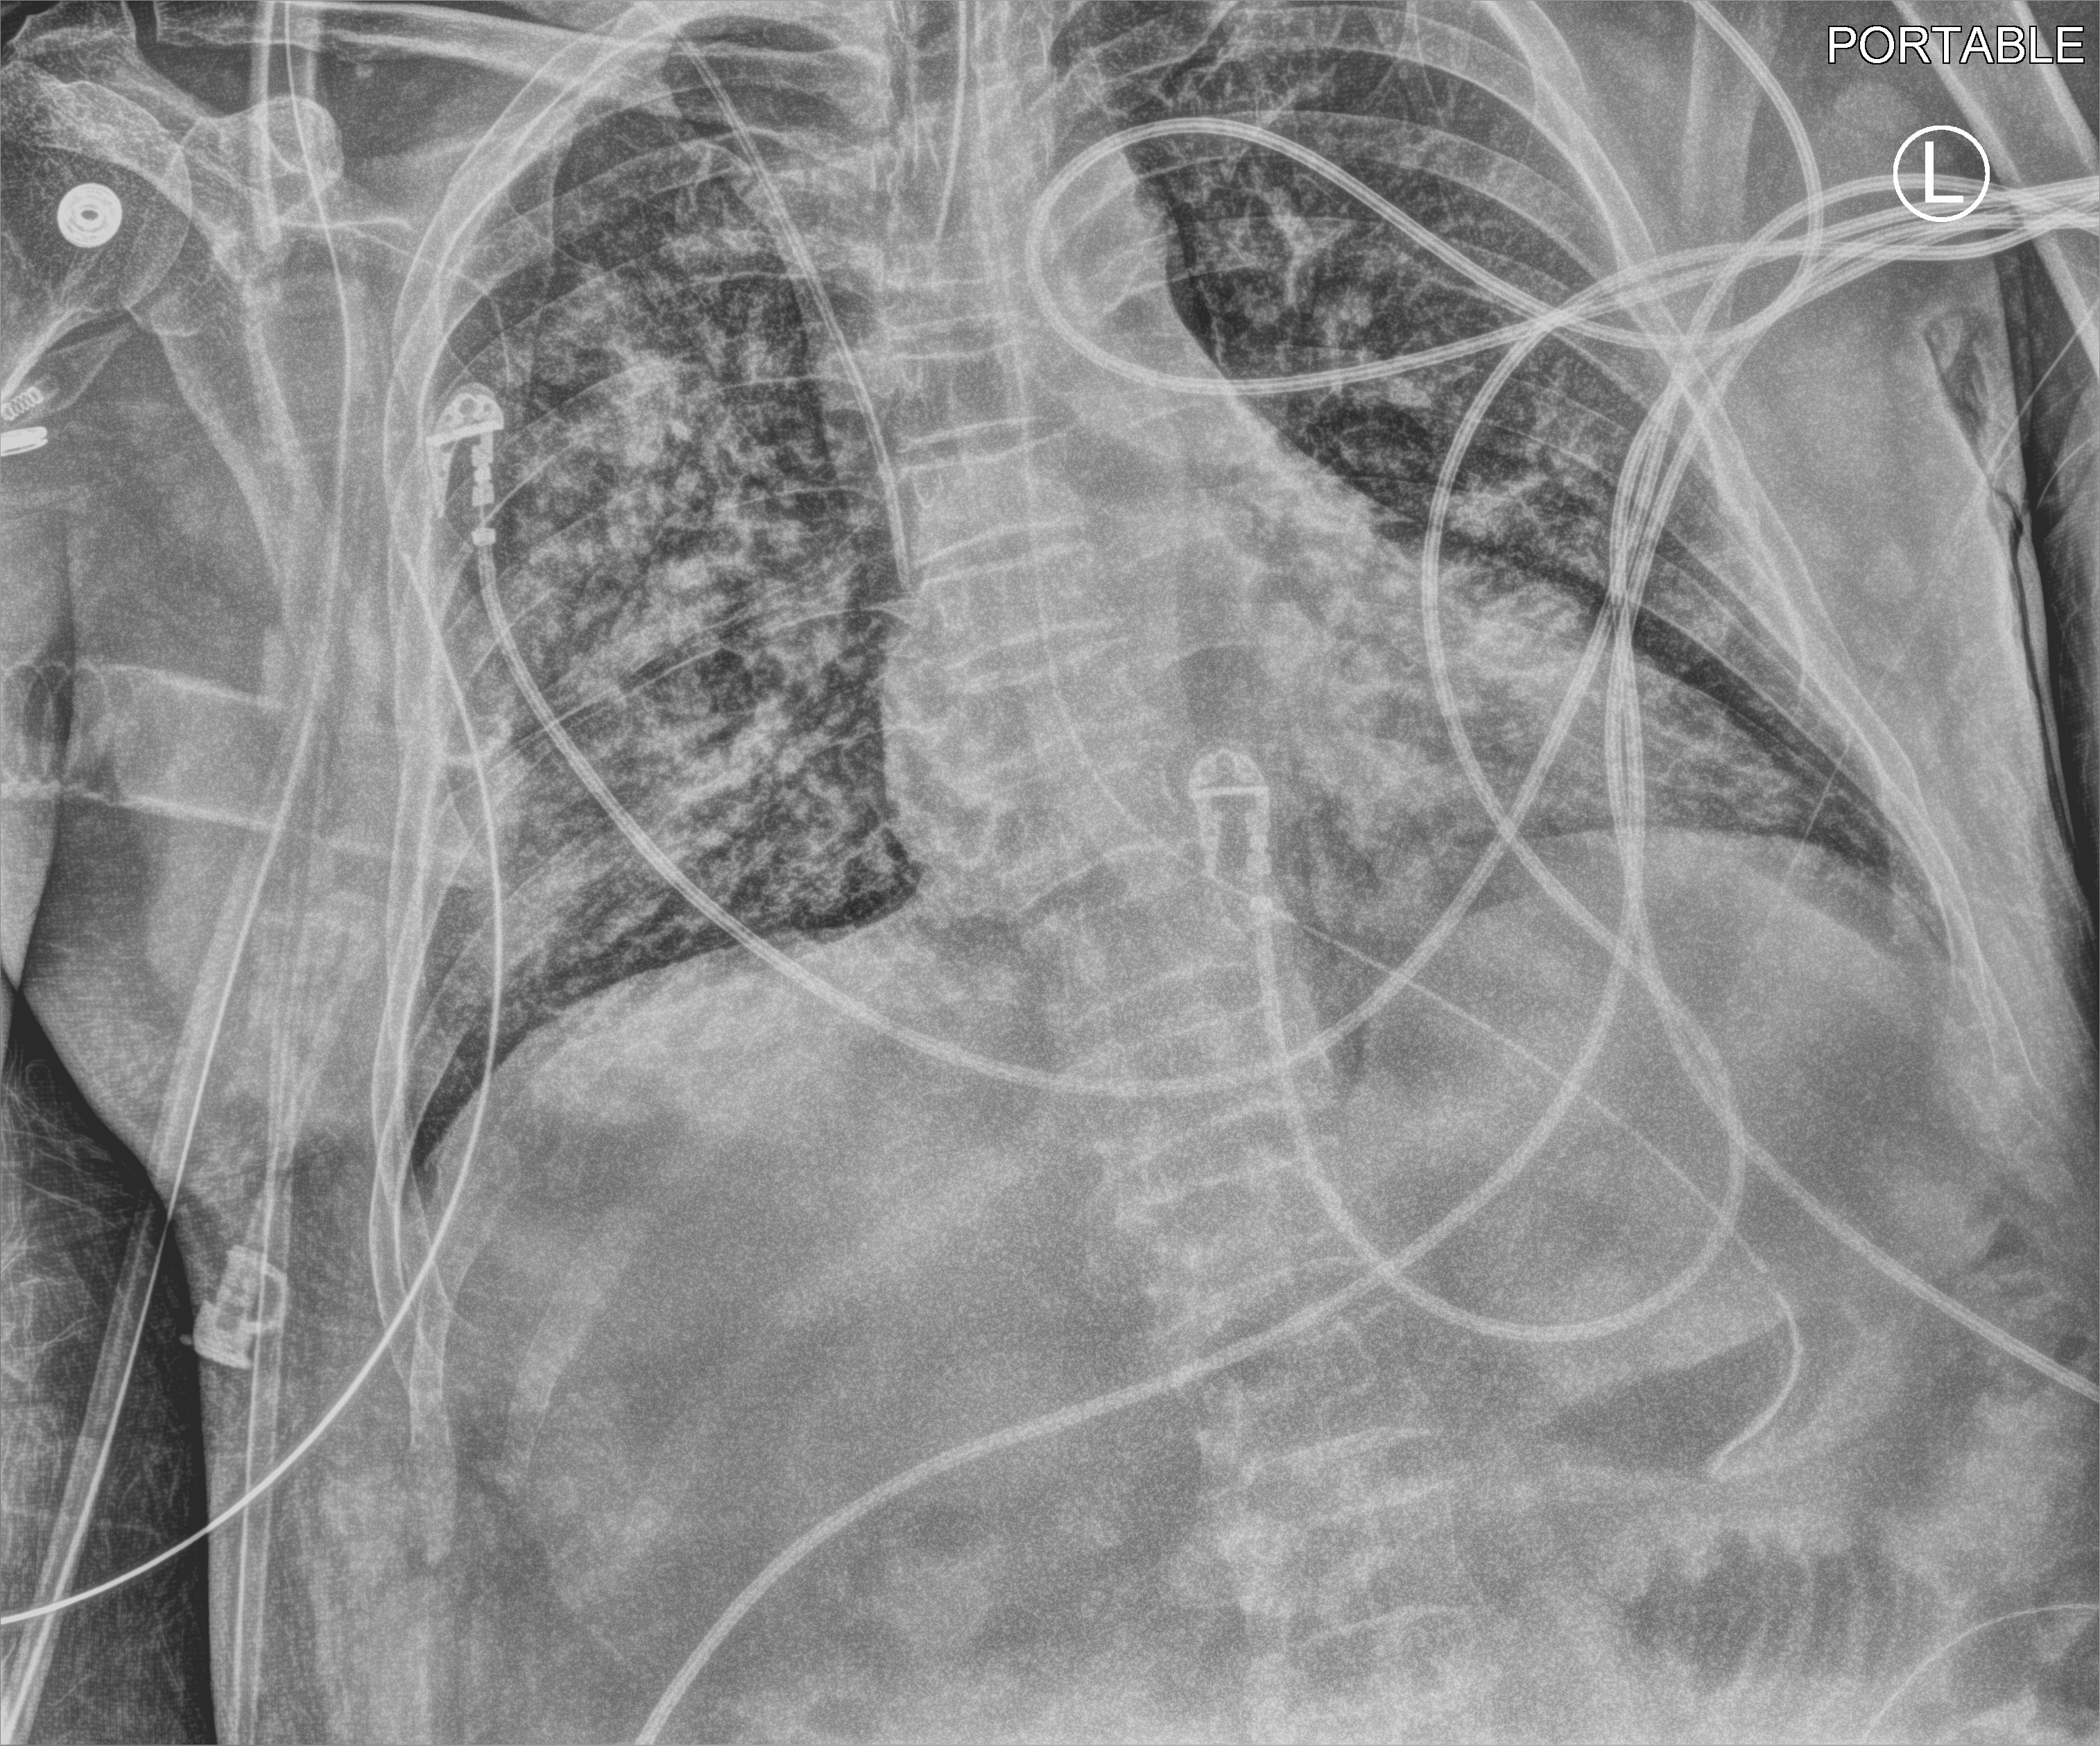
Chest X-ray (portable), anteroposterior (AP) projection. Patient hospitalised with COVID-19; male, aged 60–74 years.
Admission-level facts for this patient (not findings on this image; timing relative to this image not recorded):
- admitted to intensive care during this hospital stay: yes
- diabetes (admission record): no